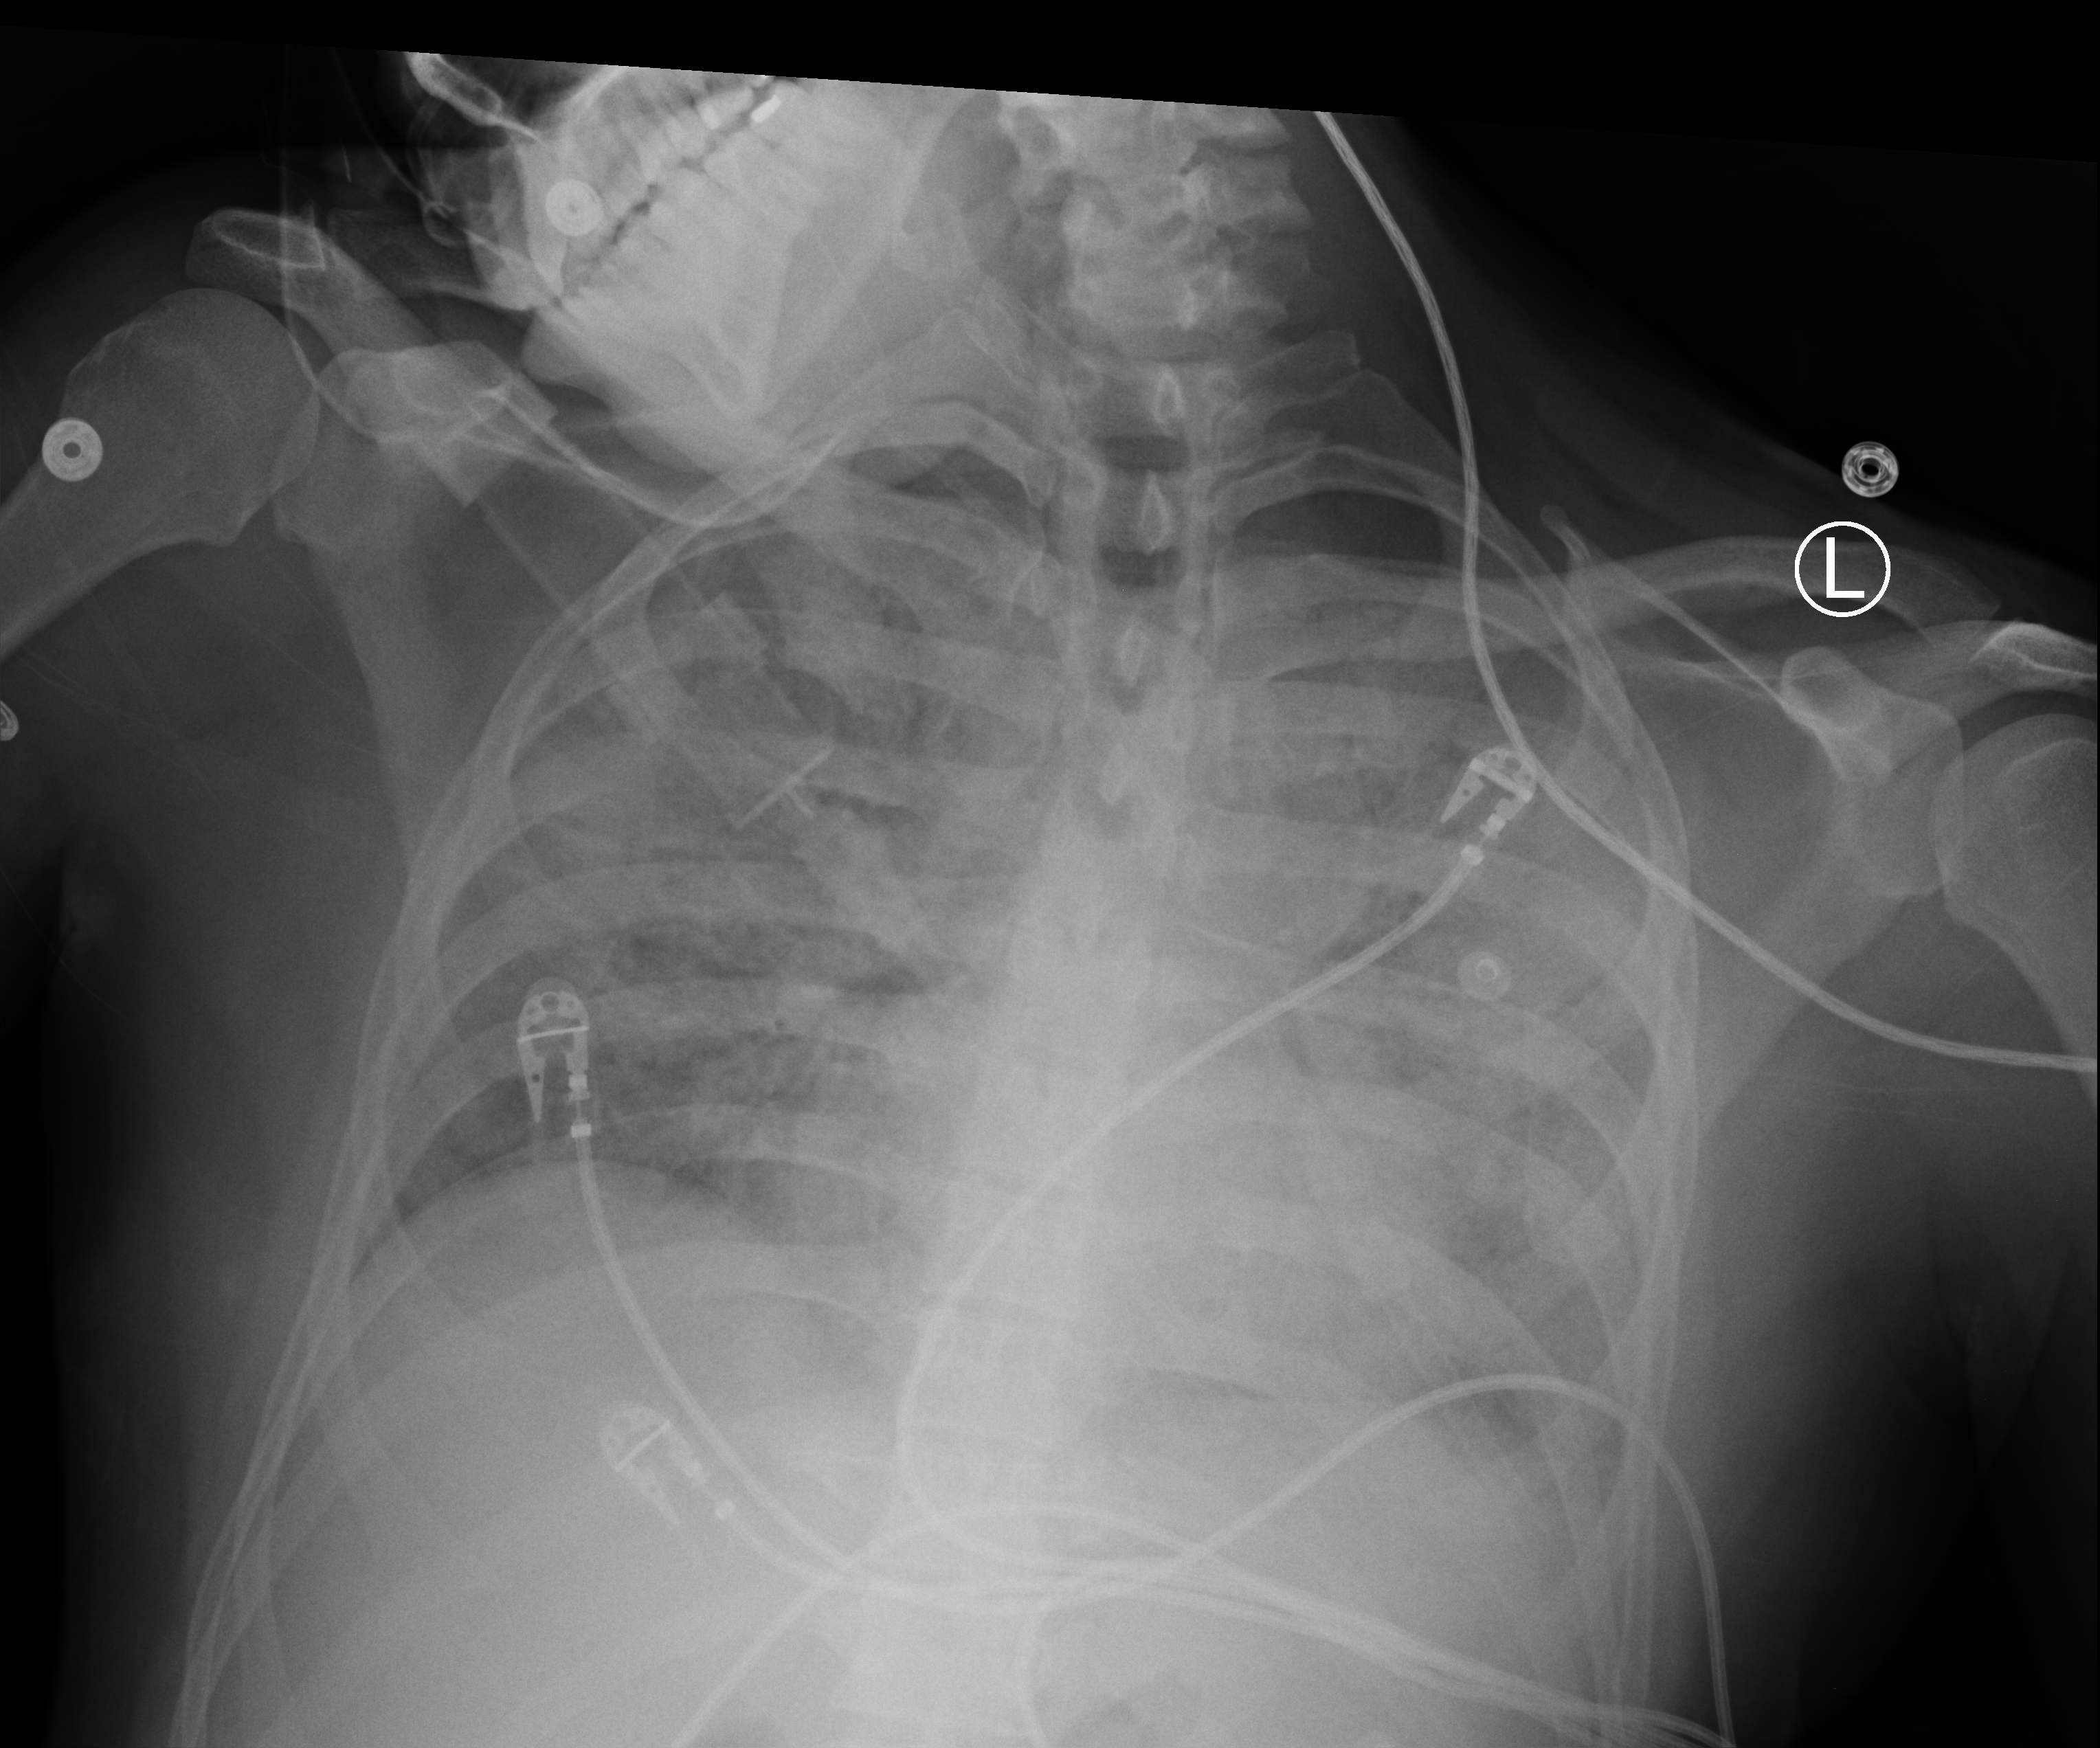
Bedside chest radiograph (computed radiography), anteroposterior (AP) projection. Patient hospitalised with COVID-19; male, aged 18–59 years.
Hospital-stay facts (about this admission, not read from this image; timing relative to this image not recorded): hypertension (admission record): no; other chronic lung disease (admission record): no; admitted to intensive care during this hospital stay: yes.